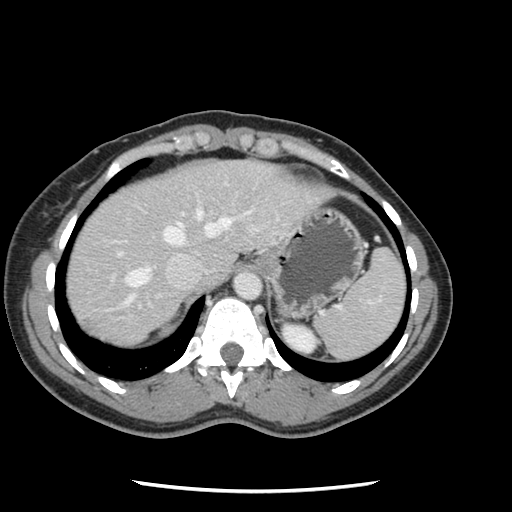
Contrast-enhanced abdominal CT, one axial slice; position 99 of 134 along the scan axis; intravenous contrast given; soft-tissue window (W 400 / L 40 HU); 2.5 mm slice thickness; 512 × 512 image matrix, field of view 330 × 330 mm. Female patient, age 43 years. From the clinical record (not read from this slice): diagnosis: colorectal cancer liver metastases, imaged before liver resection.
Annotated regions visible in this slice (manually delineated by an expert):
- hepatic veins: bounding box <123,207,251,306> (left, top, right, bottom; pixels)
- liver: <66,160,327,346>
- planned liver remnant (the part of the liver to remain after resection): <66,171,196,306>
- portal vein (with intrahepatic branches): <116,219,277,307>
- liver metastasis: <86,326,96,336>